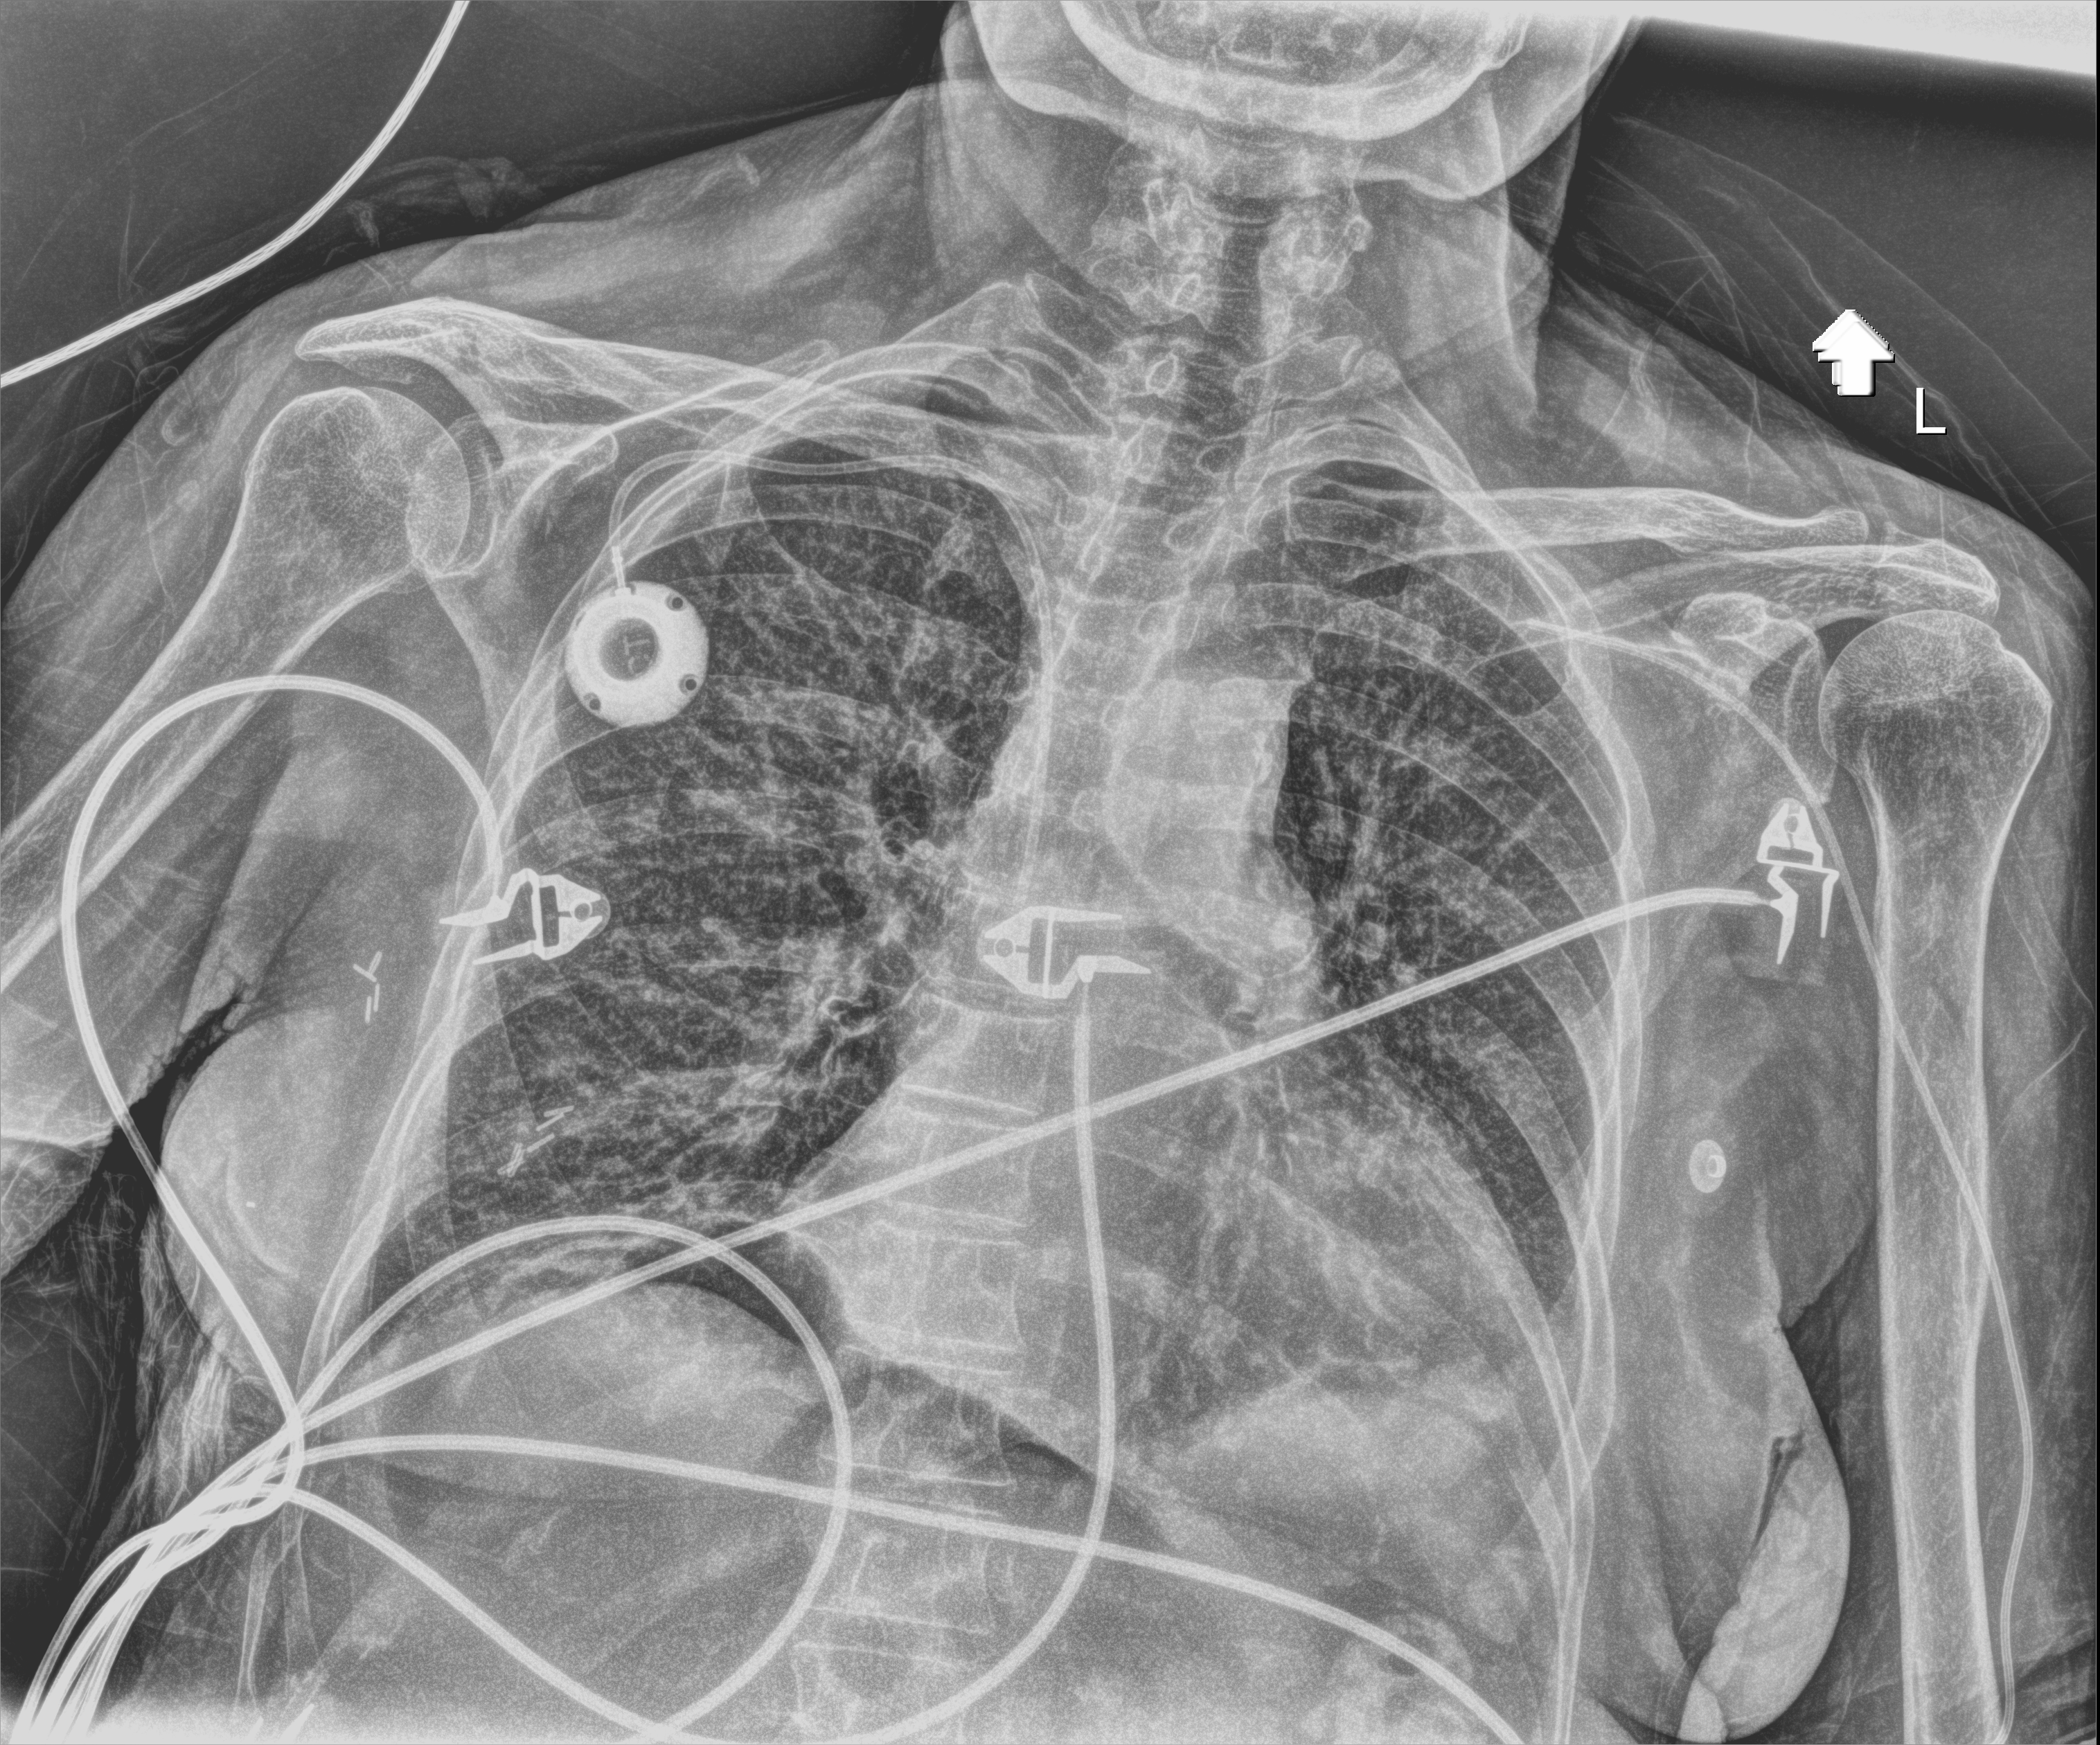
Portable chest radiograph, anteroposterior (AP) projection. Patient hospitalised with COVID-19; female, aged 60–74 years.
From the hospital-stay record, not from the radiograph (when in the stay this image was taken is not recorded): length of hospital stay: 43 days; admitted to intensive care during this hospital stay: yes; mechanically ventilated during this hospital stay: yes.